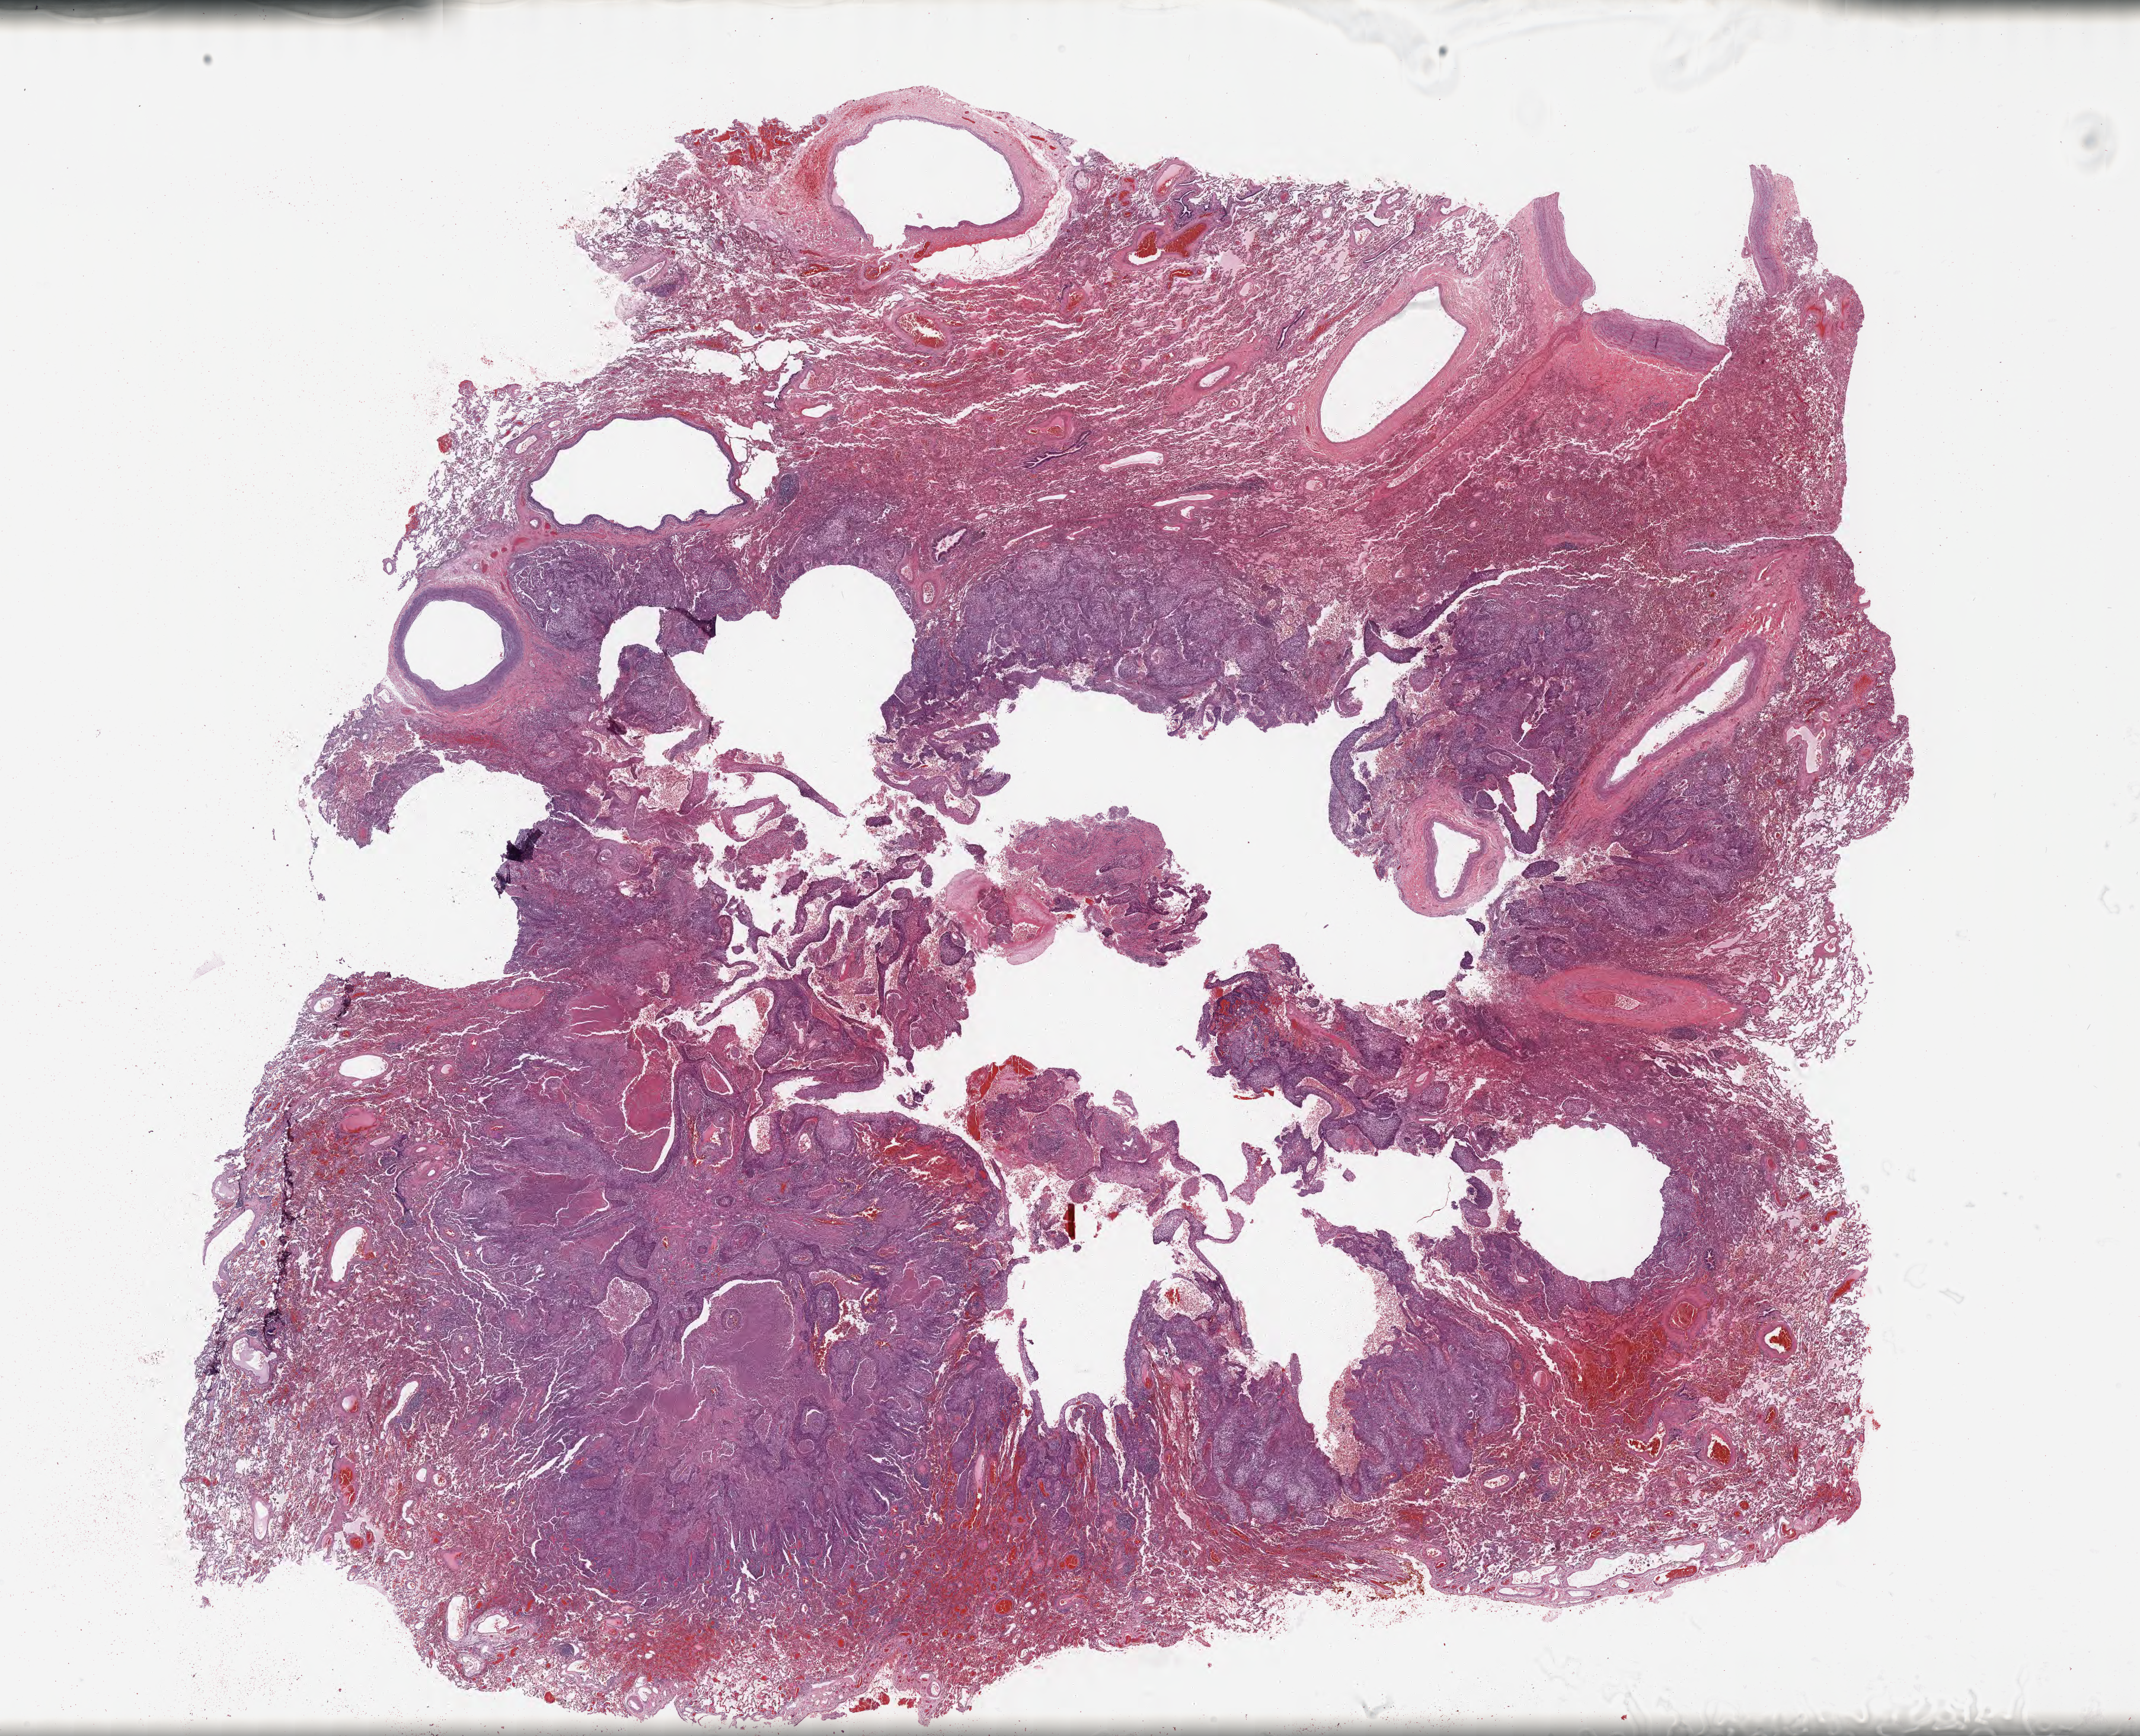
Hematoxylin and eosin (H&E) whole-slide image — a low-resolution overview of the entire scanned area, about 29.2 x 23.7 mm, specimen: tumor tissue, anatomic site: lung. Patient sex: male.
Histologic diagnosis: Squamous cell carcinoma, NOS.